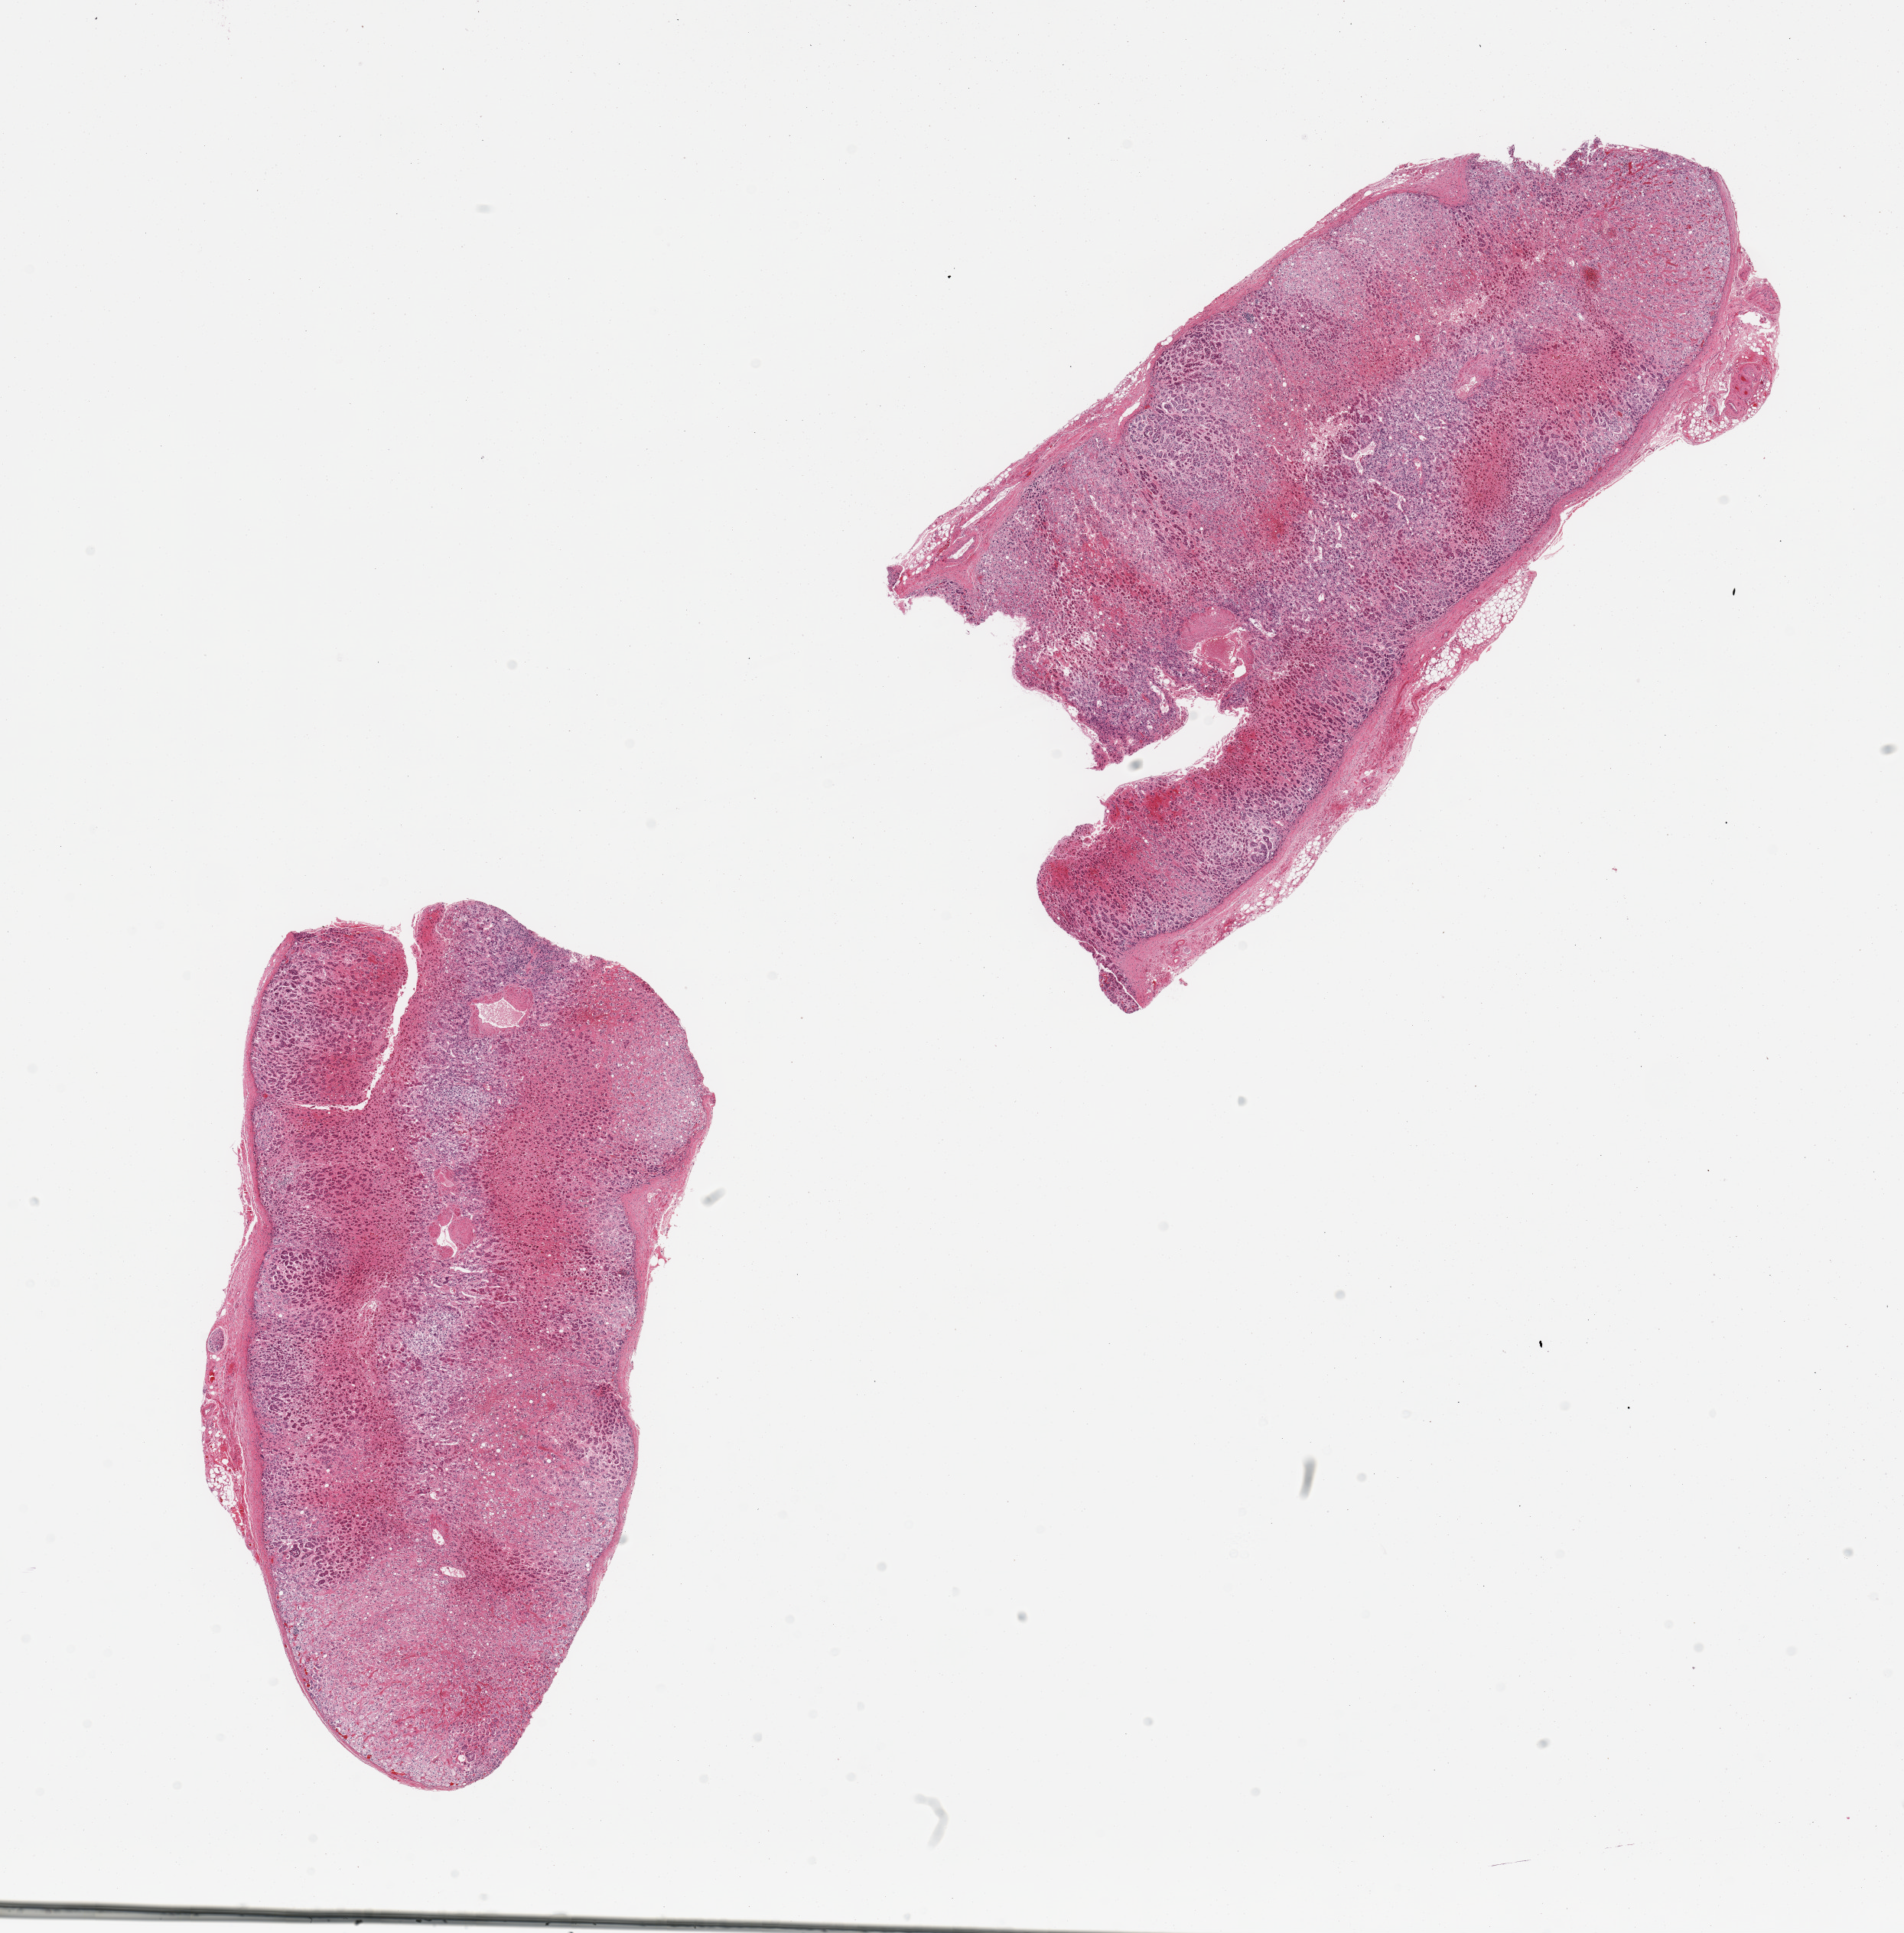
H&E whole-slide image, whole scanned area (about 19.7 x 20.0 mm) shown as a low-resolution overview; PAXgene-fixed paraffin-embedded (PFPE) section; sampled site (target tissue): adrenal gland; tissue donor sample. Male donor.
Pathologist's review note for this sample: 2 pieces, all cortex.